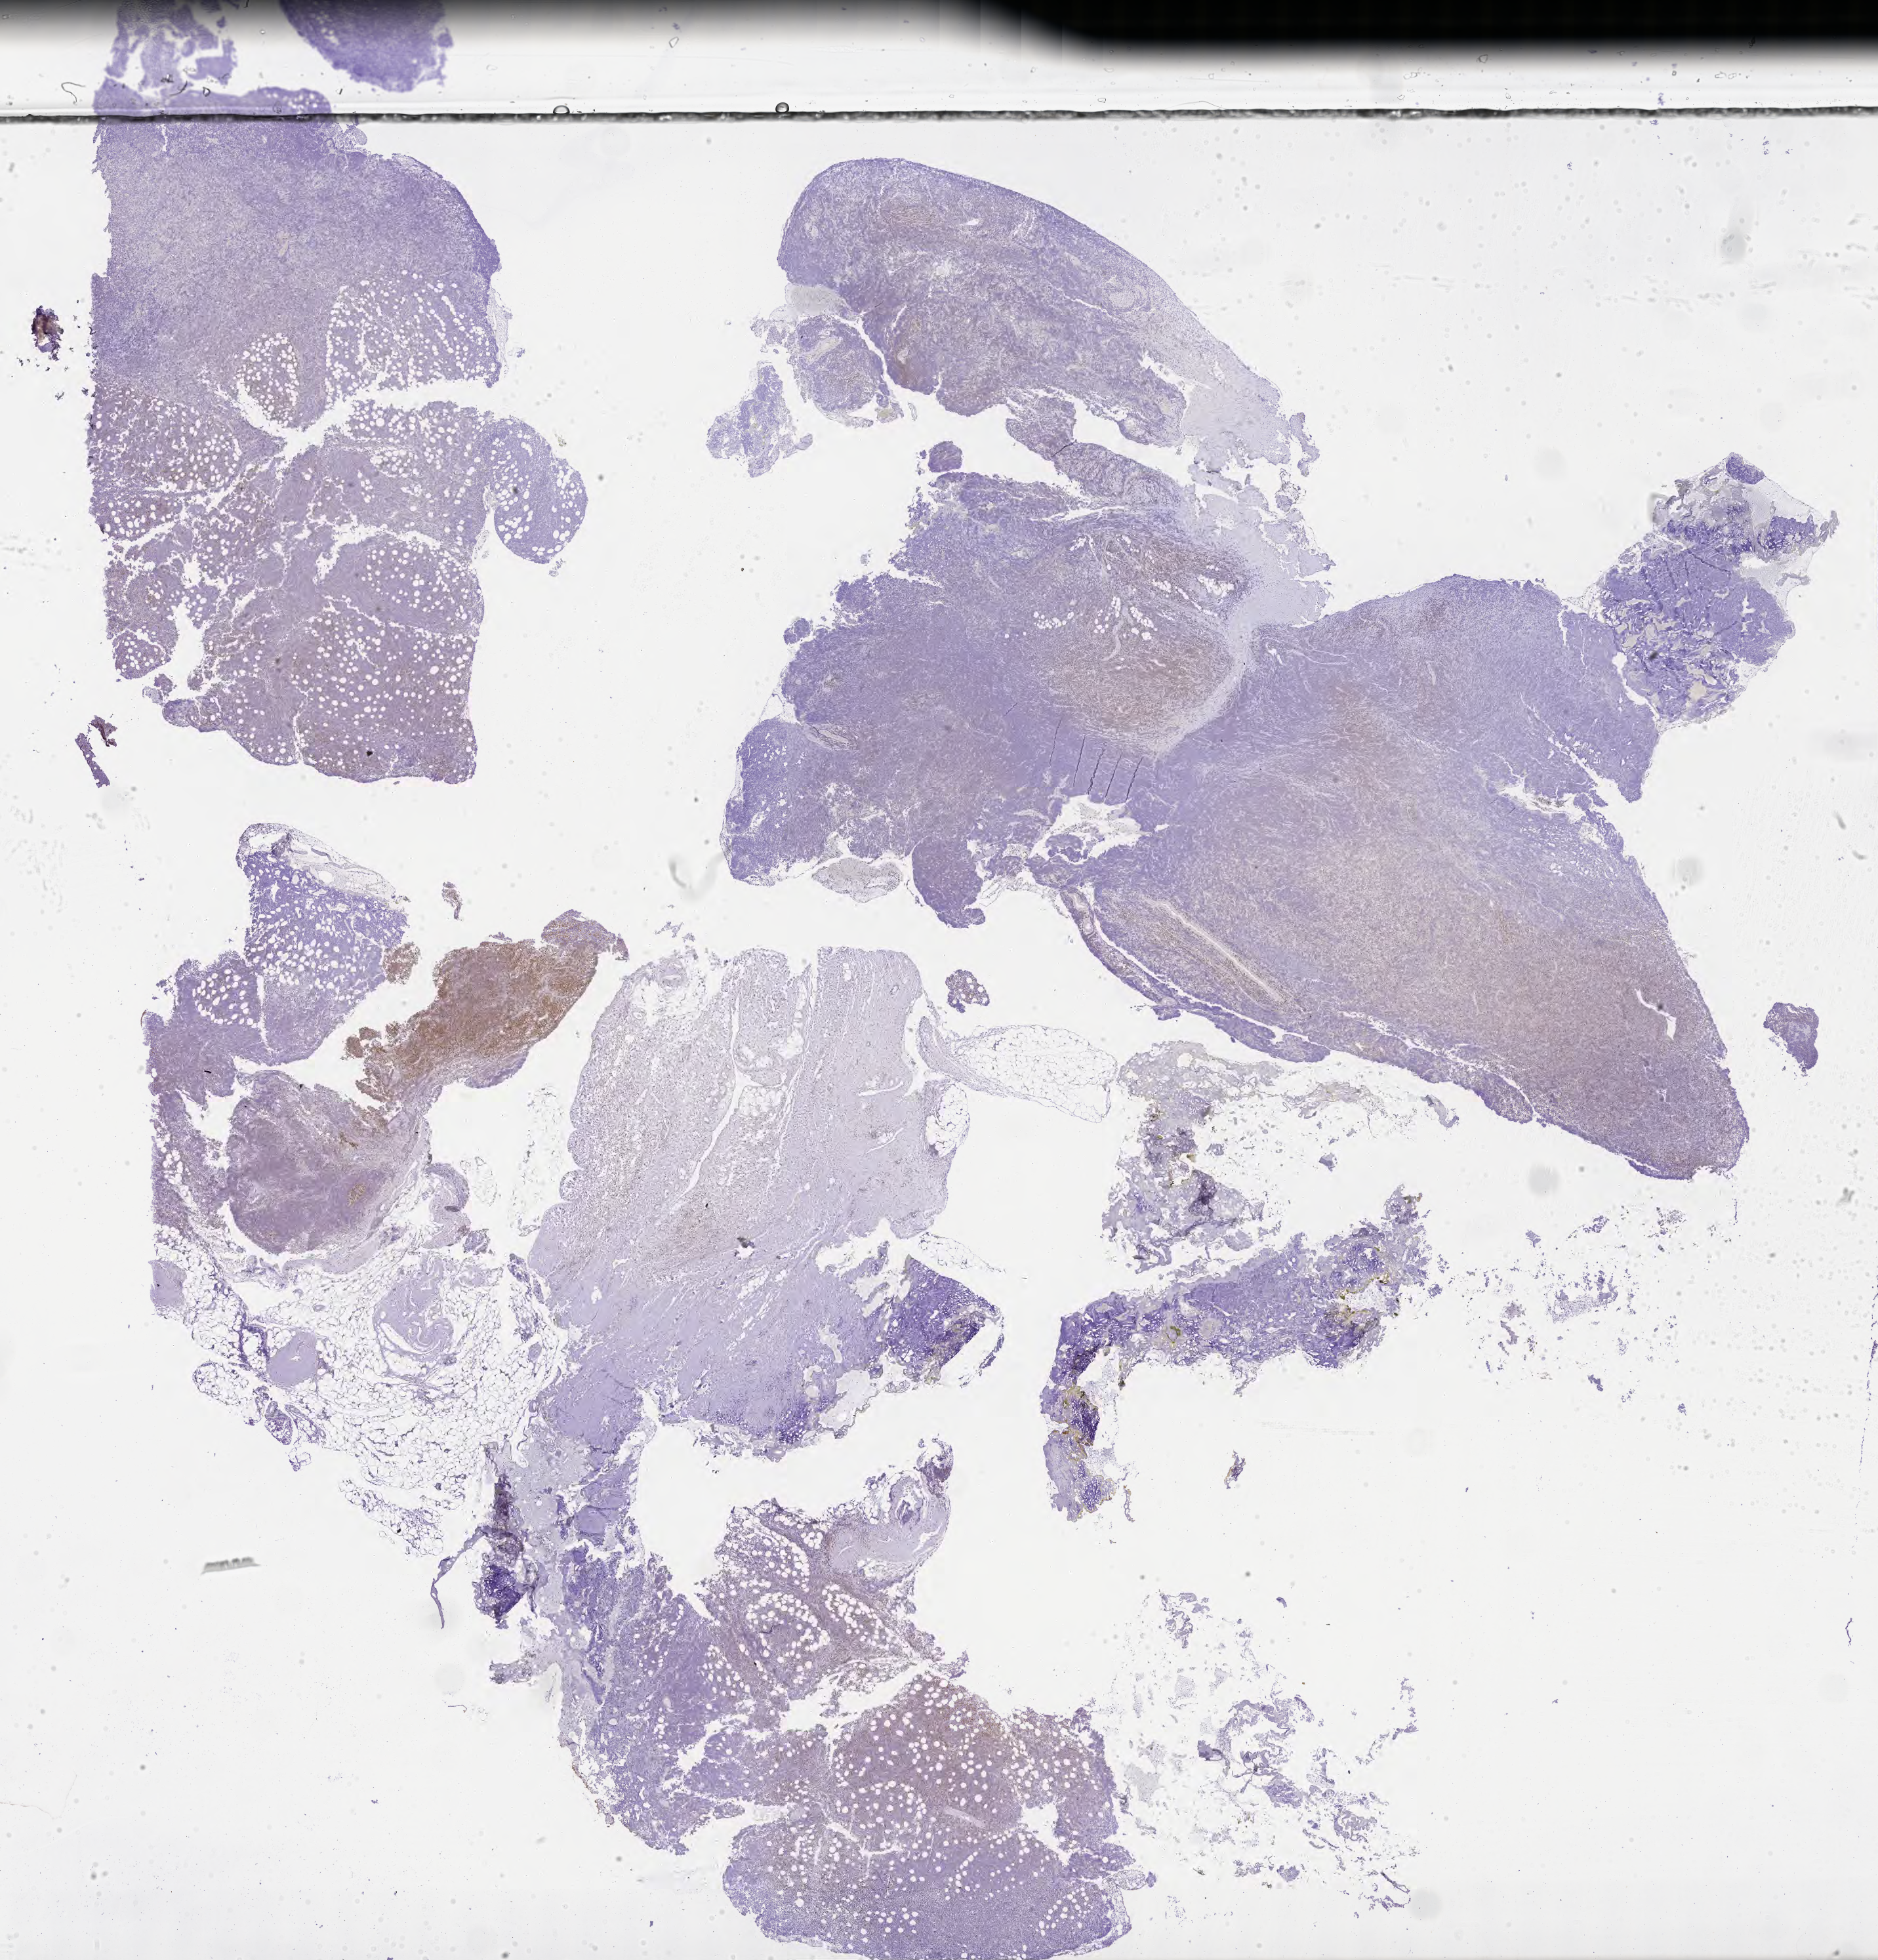
Immunohistochemistry (IHC) whole-slide image stained for BCL6 — a low-resolution overview of the entire scanned area, about 23.1 x 24.2 mm, specimen: tumor tissue. Patient: female, 72 years old.
Diagnosis: Burkitt lymphoma, NOS.